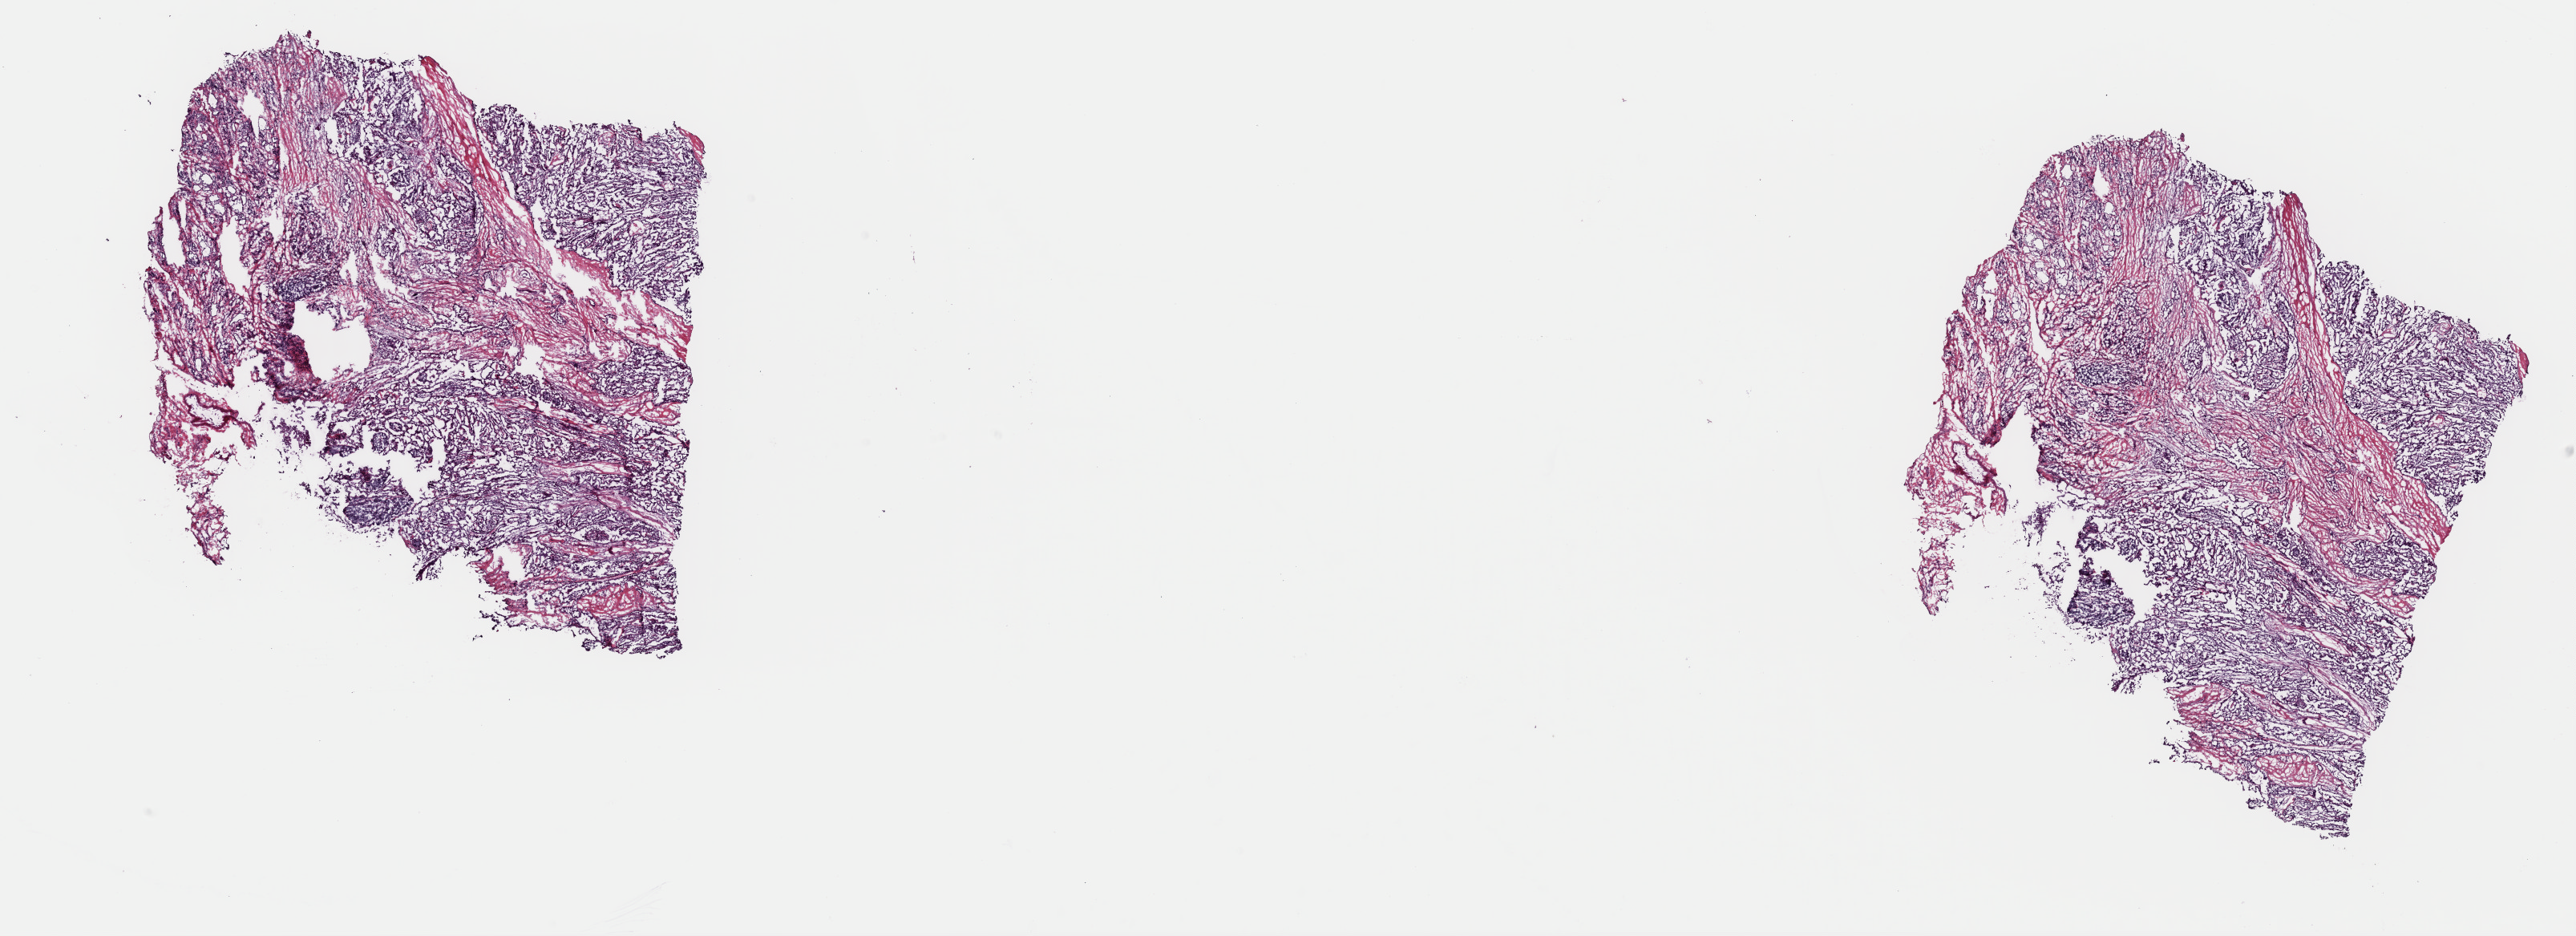
H&E-stained whole-slide image — low-resolution overview of the scanned area, about 25.4 x 9.2 mm (from a 40x scan), frozen section, primary tumour sample from the thyroid. Patient: female, age at initial diagnosis 38 years.
Histologic diagnosis: Papillary adenocarcinoma, NOS (thyroid gland).